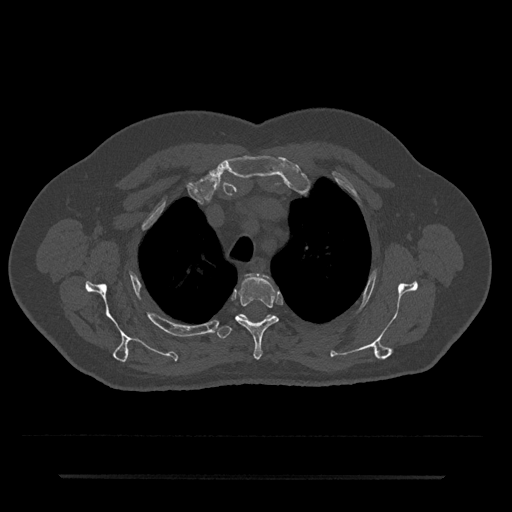
CT including the spine, one axial slice. 120 kVp. Bone window (W 1800 / L 400 HU). 512 × 512 image matrix. Male patient, age 69 years. Case-level facts recorded for this patient, not image findings: primary cancer: prostate.
Structures marked on this image (semi-automatic segmentation, software-assisted and operator-edited):
- T3 vertebra: box from (x=235, y=276) to (x=279, y=360) px
- T4 vertebra: (x=217, y=315)–(x=271, y=339)